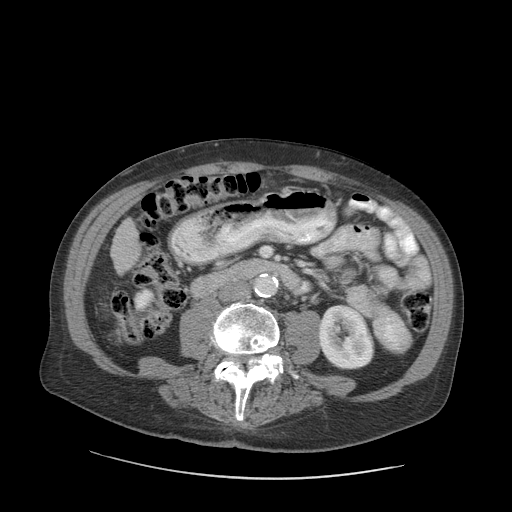
Contrast-enhanced abdominal CT (liver protocol), one axial slice; position 20 of 89 along the scan axis; reconstruction kernel STANDARD; 140 kVp; soft-tissue window (W 400 / L 40 HU); 2.5 mm slice thickness; 512 × 512 image matrix, field of view 420 × 420 mm. Case-level facts recorded for this patient, not image findings: diagnosis: hepatocellular carcinoma (patient treated with transarterial chemoembolisation; whether this scan precedes or follows treatment is not stated here); TNM stage (as recorded): Stage-I; Child-Pugh class: A; tumour differentiation: moderately differentiated.
Annotated regions visible in this slice (semi-automatically segmented with operator editing):
- liver parenchyma outside the tumour (the mass and vessels are separate outlines, so this box may not span the whole liver): bounding box <110,218,140,274> (left, top, right, bottom; pixels)